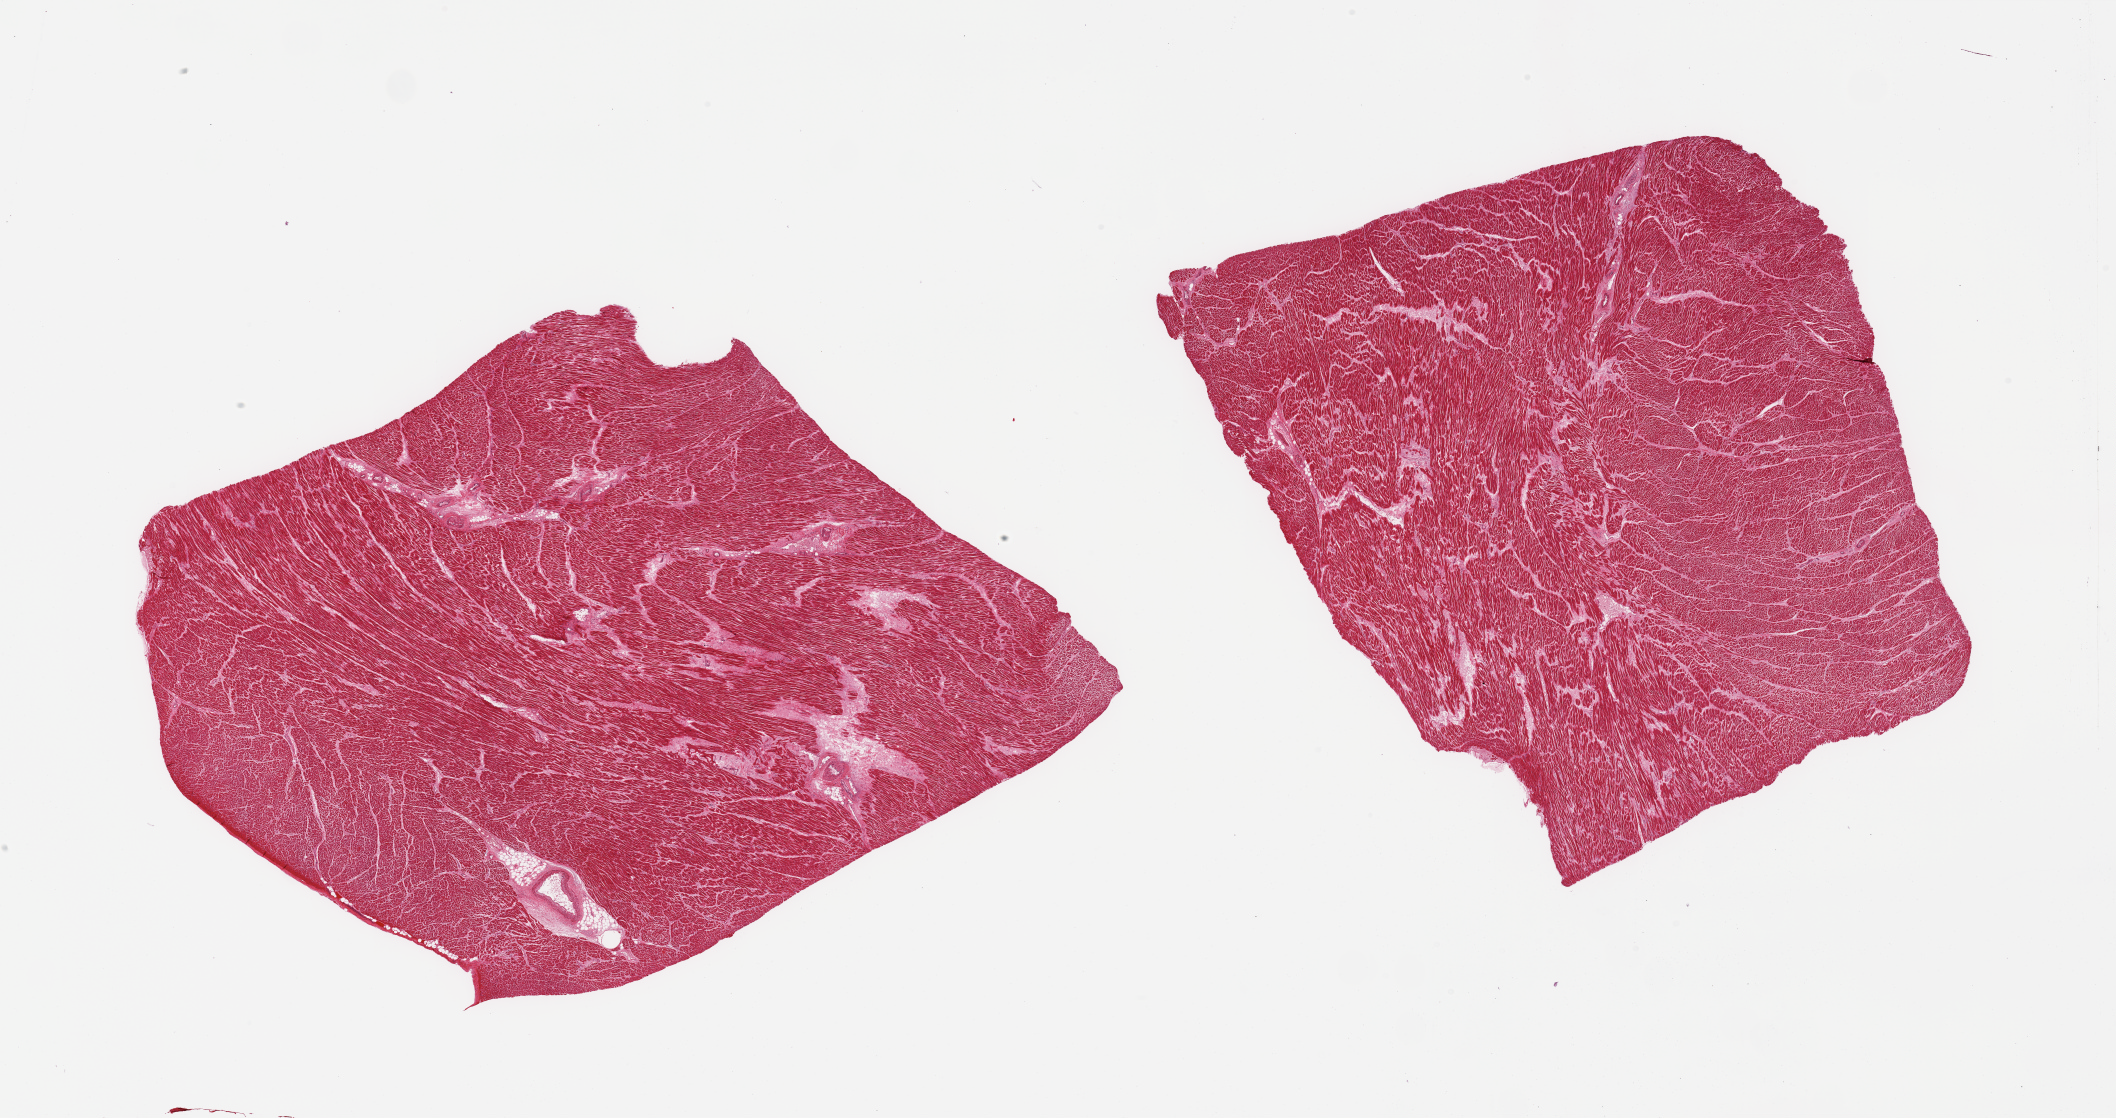
Digitized haematoxylin and eosin-stained section — low-resolution overview of the scanned area, about 33.5 x 17.7 mm (slide scanned at 20x). PAXgene-fixed paraffin-embedded (PFPE) section. Section of heart (target tissue). Tissue donor sample. Male donor.
Review note (as recorded): 2 pieces; fatty degeneration with mild to moderate autolysis of the interstitial fat; congested capillaries.